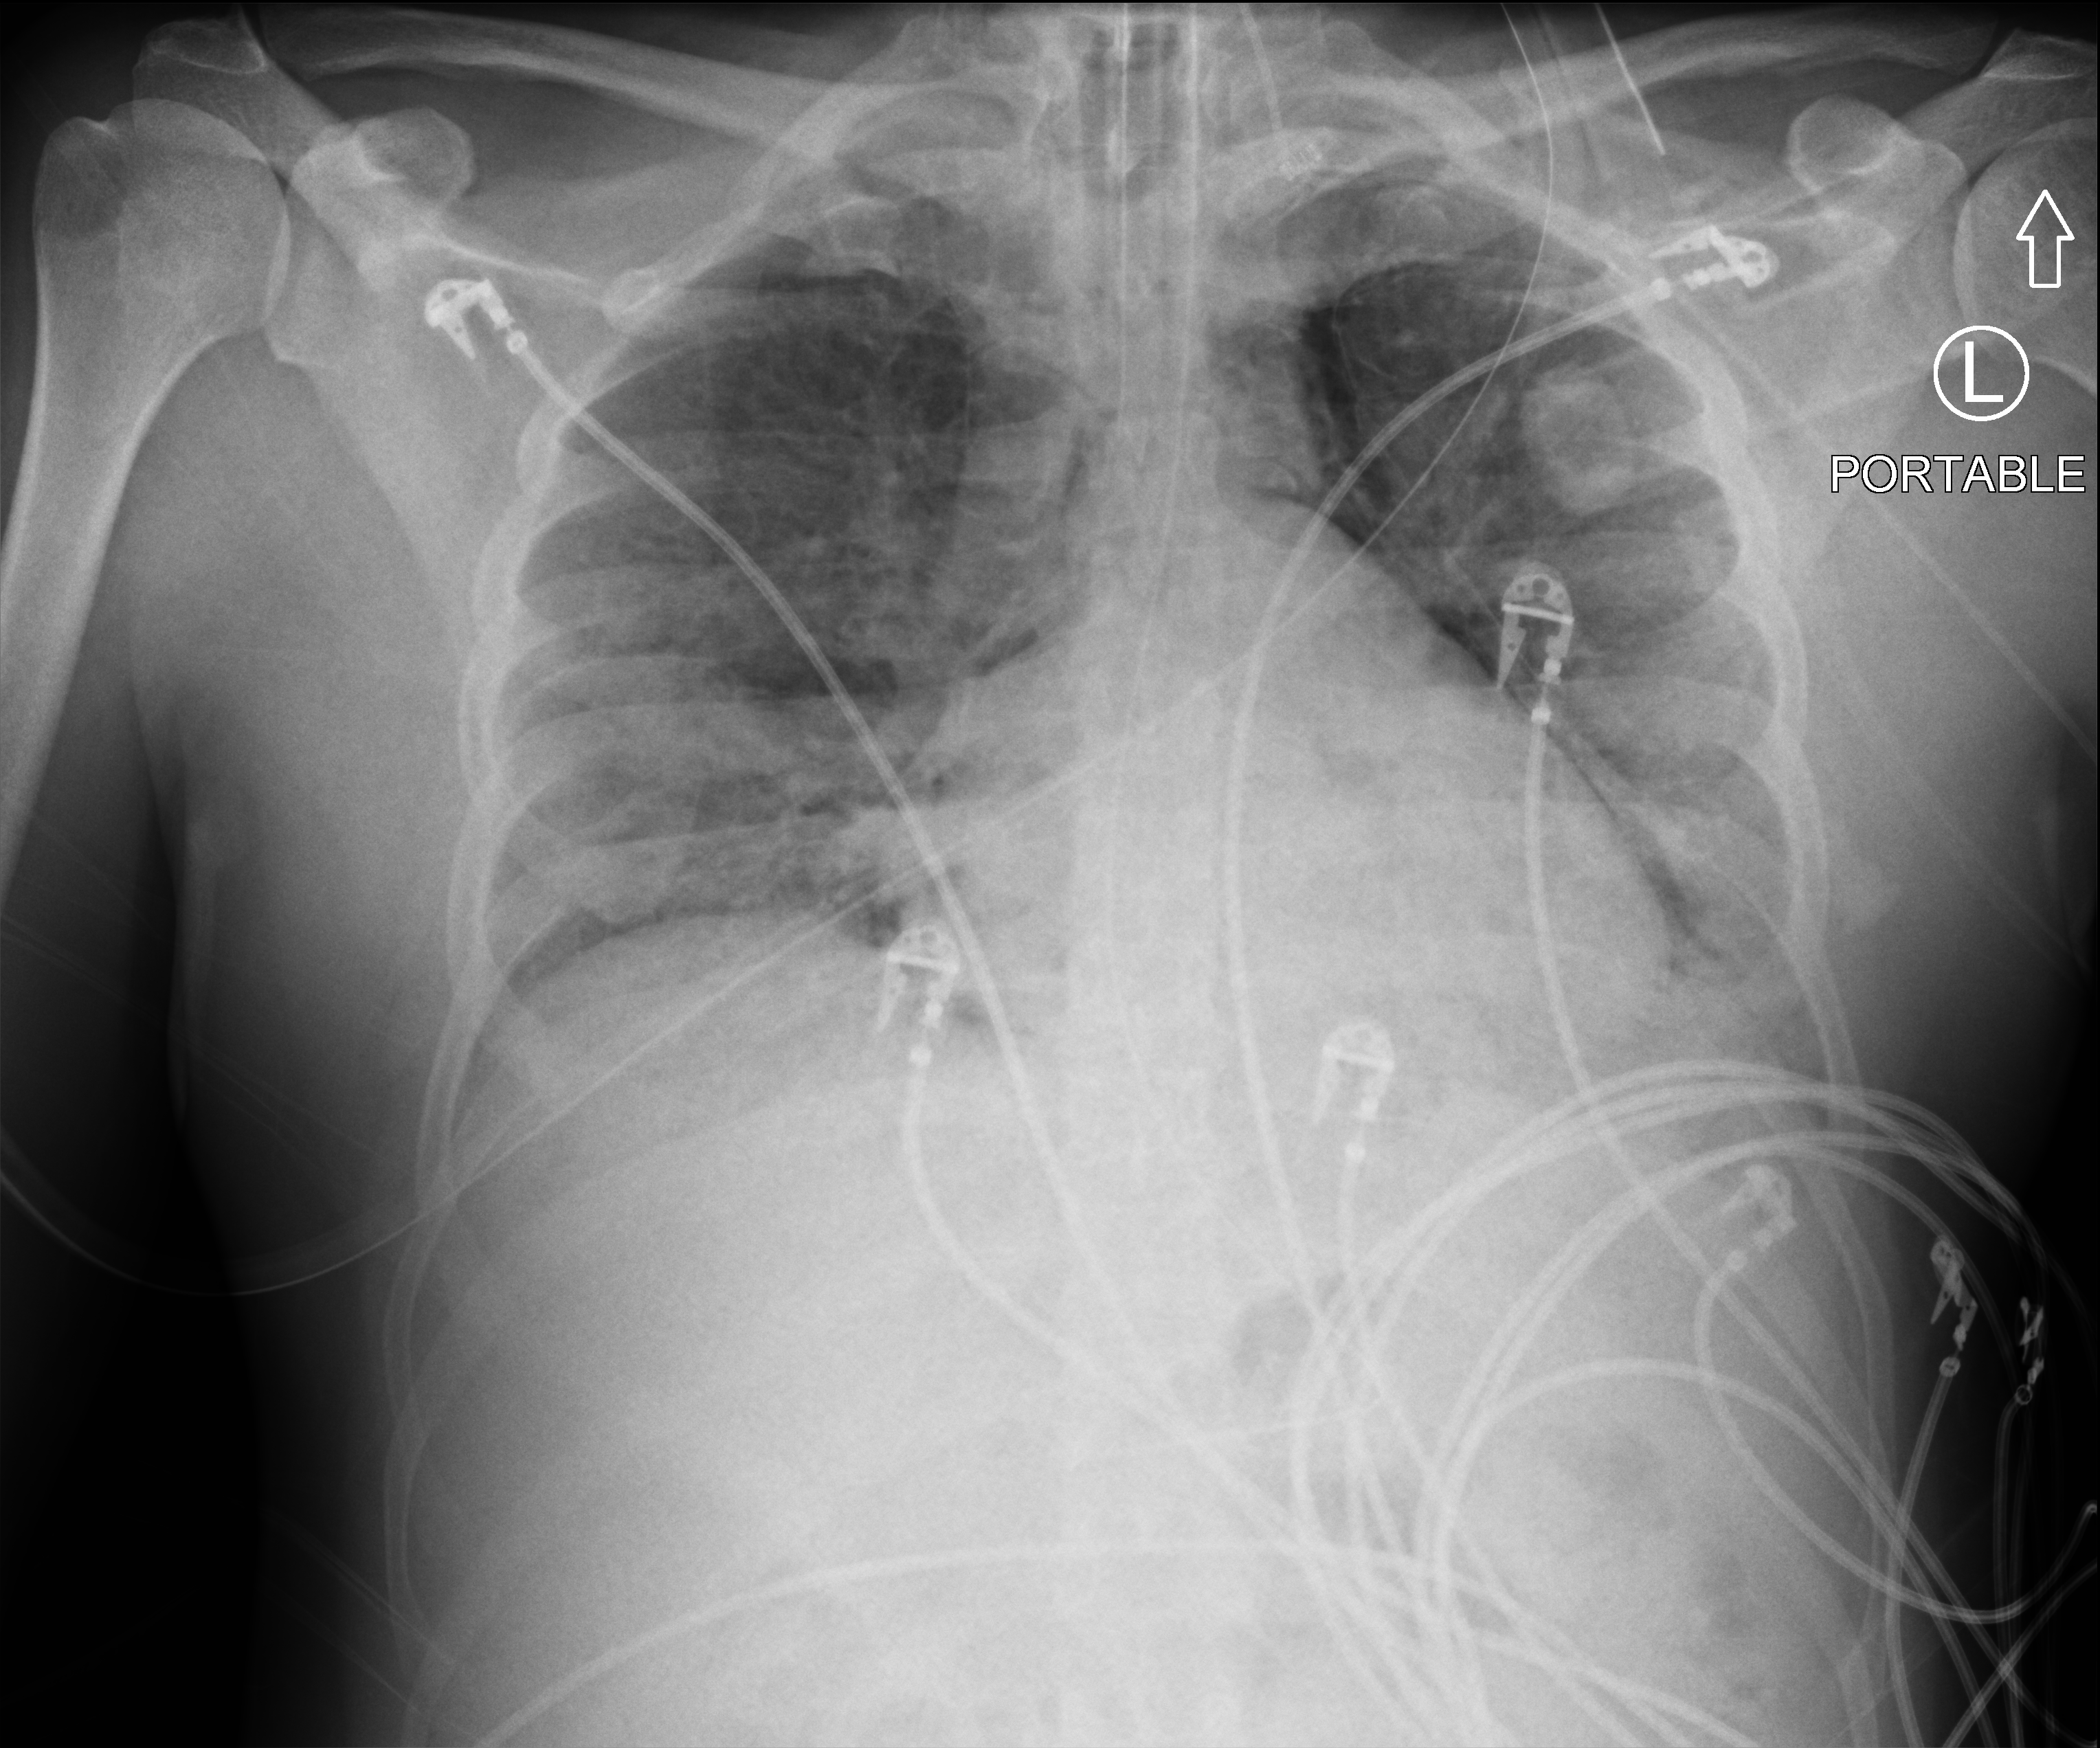
Portable chest radiograph, anteroposterior (AP) projection. Male patient hospitalised with COVID-19, age 18–59 years.
Admission-level facts for this patient (not findings on this image; timing relative to this image not recorded): length of hospital stay: 30 days; other chronic lung disease (admission record): no.